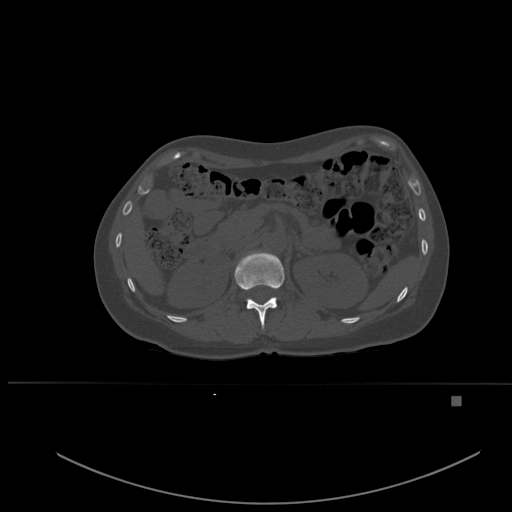
CT including the spine, one axial slice. Slice 250 of 651 in the series (ordered by position). Bone window (W 1800 / L 400 HU). 1.5 mm slice thickness. 512 × 512 image matrix, field of view 443 × 443 mm. Female patient, age 49 years. Case-level facts recorded for this patient, not image findings: primary cancer: breast; vertebrae with lytic lesions (as recorded): L3, T12, L4.
Outlined on this slice (semi-automatic segmentation, software-assisted and operator-edited):
- T12 vertebra: bounding box <235,251,285,330> (left, top, right, bottom; pixels)